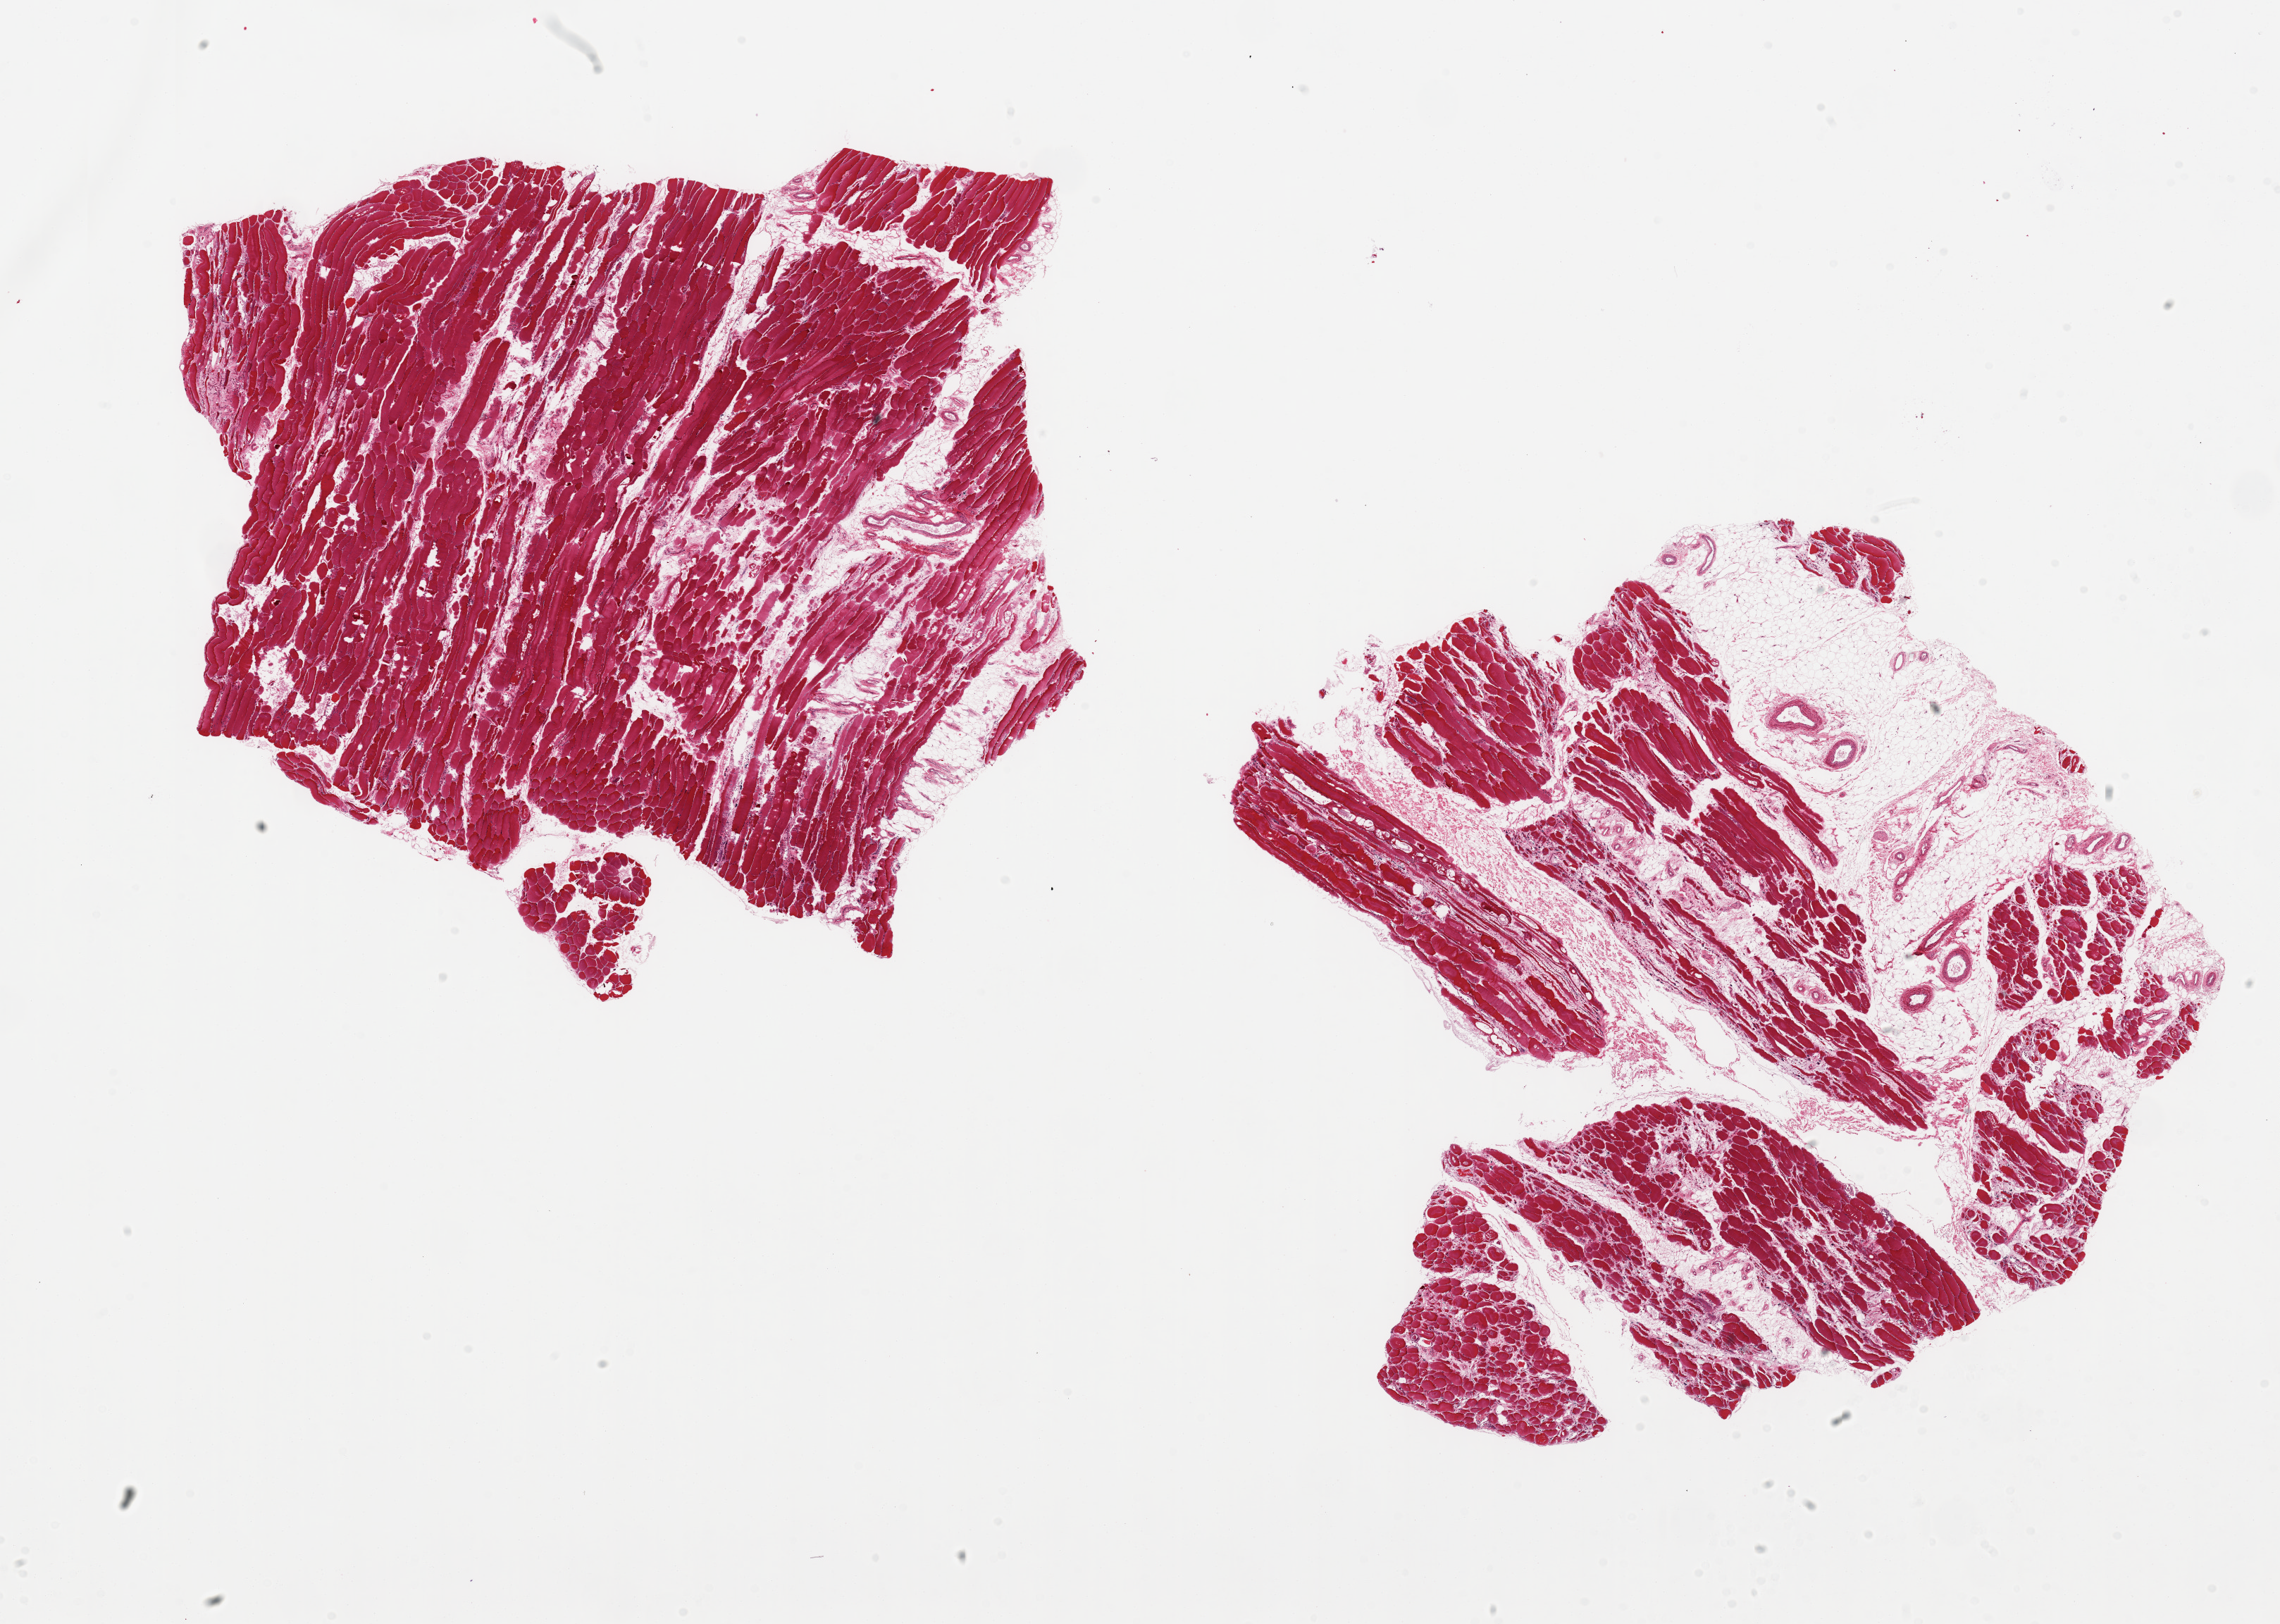
Digitized H&E-stained section — low-resolution overview of the scanned area, about 25.6 x 18.2 mm (acquisition: 20x scan); PAXgene-fixed, paraffin-embedded tissue; section of skeletal muscle (target tissue); donor tissue sample.
Pathologist's review note for this sample: 2 pieces 10x10 & 11x8 mm; moderate to severe atrophy and vacuolar degeneration; ~40% adipose in one aliquot; <10% in the other.